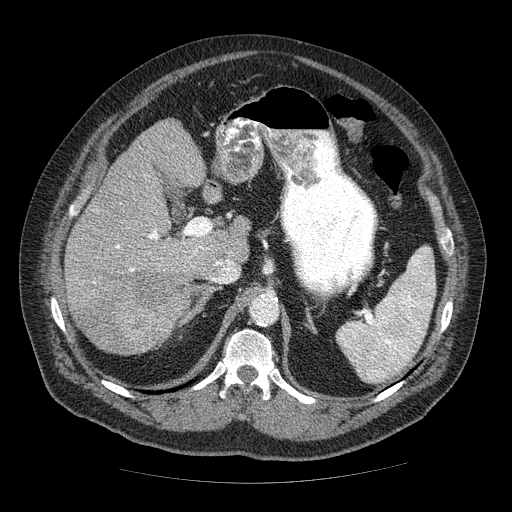
Contrast-enhanced abdominal CT (liver protocol), one axial slice; slice 34 of 85 in the series (ordered by position); soft-tissue window (W 400 / L 40 HU); 2.5 mm slice thickness; 512 × 512 image matrix. From the clinical record (not read from this slice): diagnosis: hepatocellular carcinoma (patient treated with transarterial chemoembolisation; whether this scan precedes or follows treatment is not stated here); TNM stage (as recorded): Stage-IIIA; Child-Pugh class: A; tumour size: 7 cm.
Outlined on this slice (semi-automatic segmentation, software-assisted and operator-edited):
- liver parenchyma outside the tumour (the mass and vessels are separate outlines, so this box may not span the whole liver): box from (x=64, y=120) to (x=249, y=350) px
- mass: (x=74, y=267)–(x=193, y=355)
- liver vessels: (x=116, y=229)–(x=231, y=272)